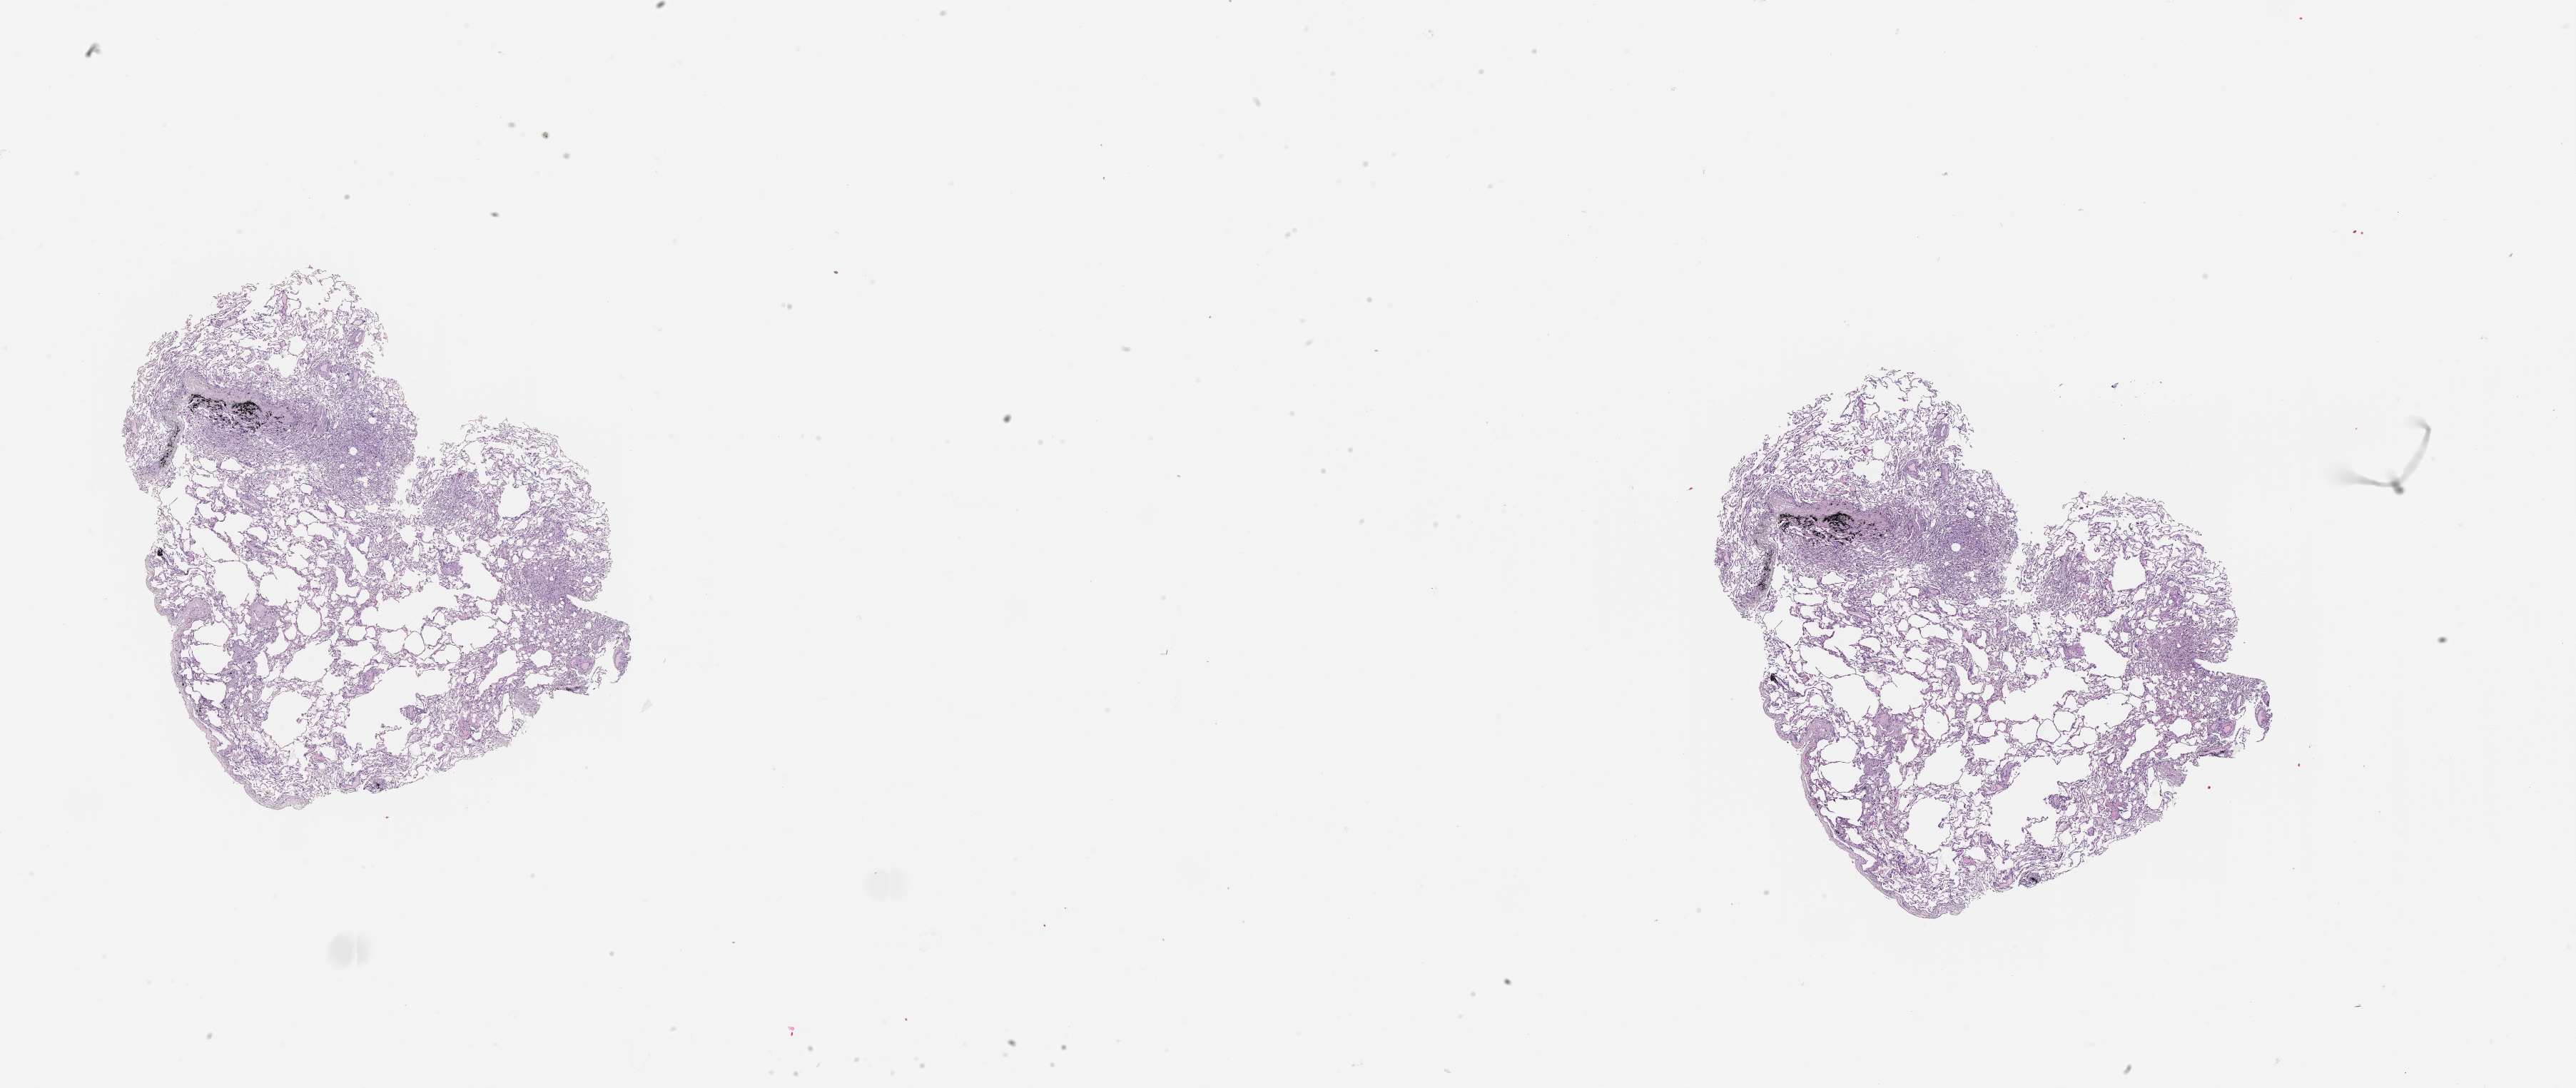
Digitized H&E-stained tissue section (whole slide) — low-resolution overview of the scanned area, about 29.1 x 12.3 mm; normal (non-tumour) tissue sample, sampled site: lung. Patient: male, age 67 years.
This section: normal (non-tumour) tissue from the same patient. Patient diagnosis: Adenocarcinoma, NOS.